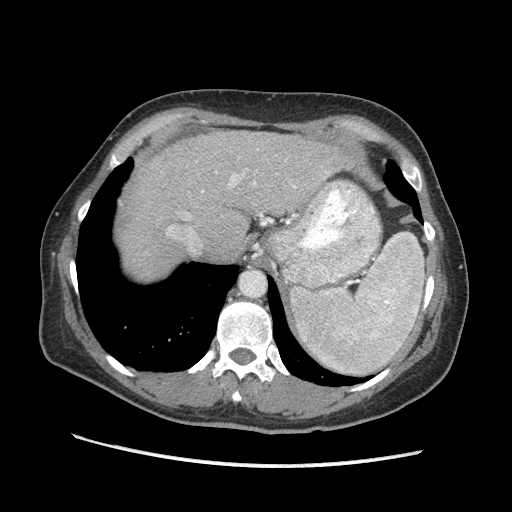
Contrast-enhanced abdominal CT (liver protocol), one axial slice. Slice 148 of 170 in the series (ordered by position). Reconstruction kernel STANDARD. Soft-tissue window (W 400 / L 40 HU). 512 × 512 image matrix, field of view 360 × 360 mm. From the clinical record (not read from this slice): diagnosis: hepatocellular carcinoma (patient treated with transarterial chemoembolisation; whether this scan precedes or follows treatment is not stated here); TNM stage (as recorded): Stage-II; Child-Pugh class: A; tumour differentiation: no biopsy; tumour size: 4 cm.
Structures marked on this image (semi-automatically segmented with operator editing):
- abdominal aorta: bounding box (x1, y1, x2, y2) in pixels: (241, 271, 264, 297)
- liver parenchyma outside the tumour (the mass and vessels are separate outlines, so this box may not span the whole liver): (118, 130, 366, 278)
- liver vessels: (168, 172, 328, 231)